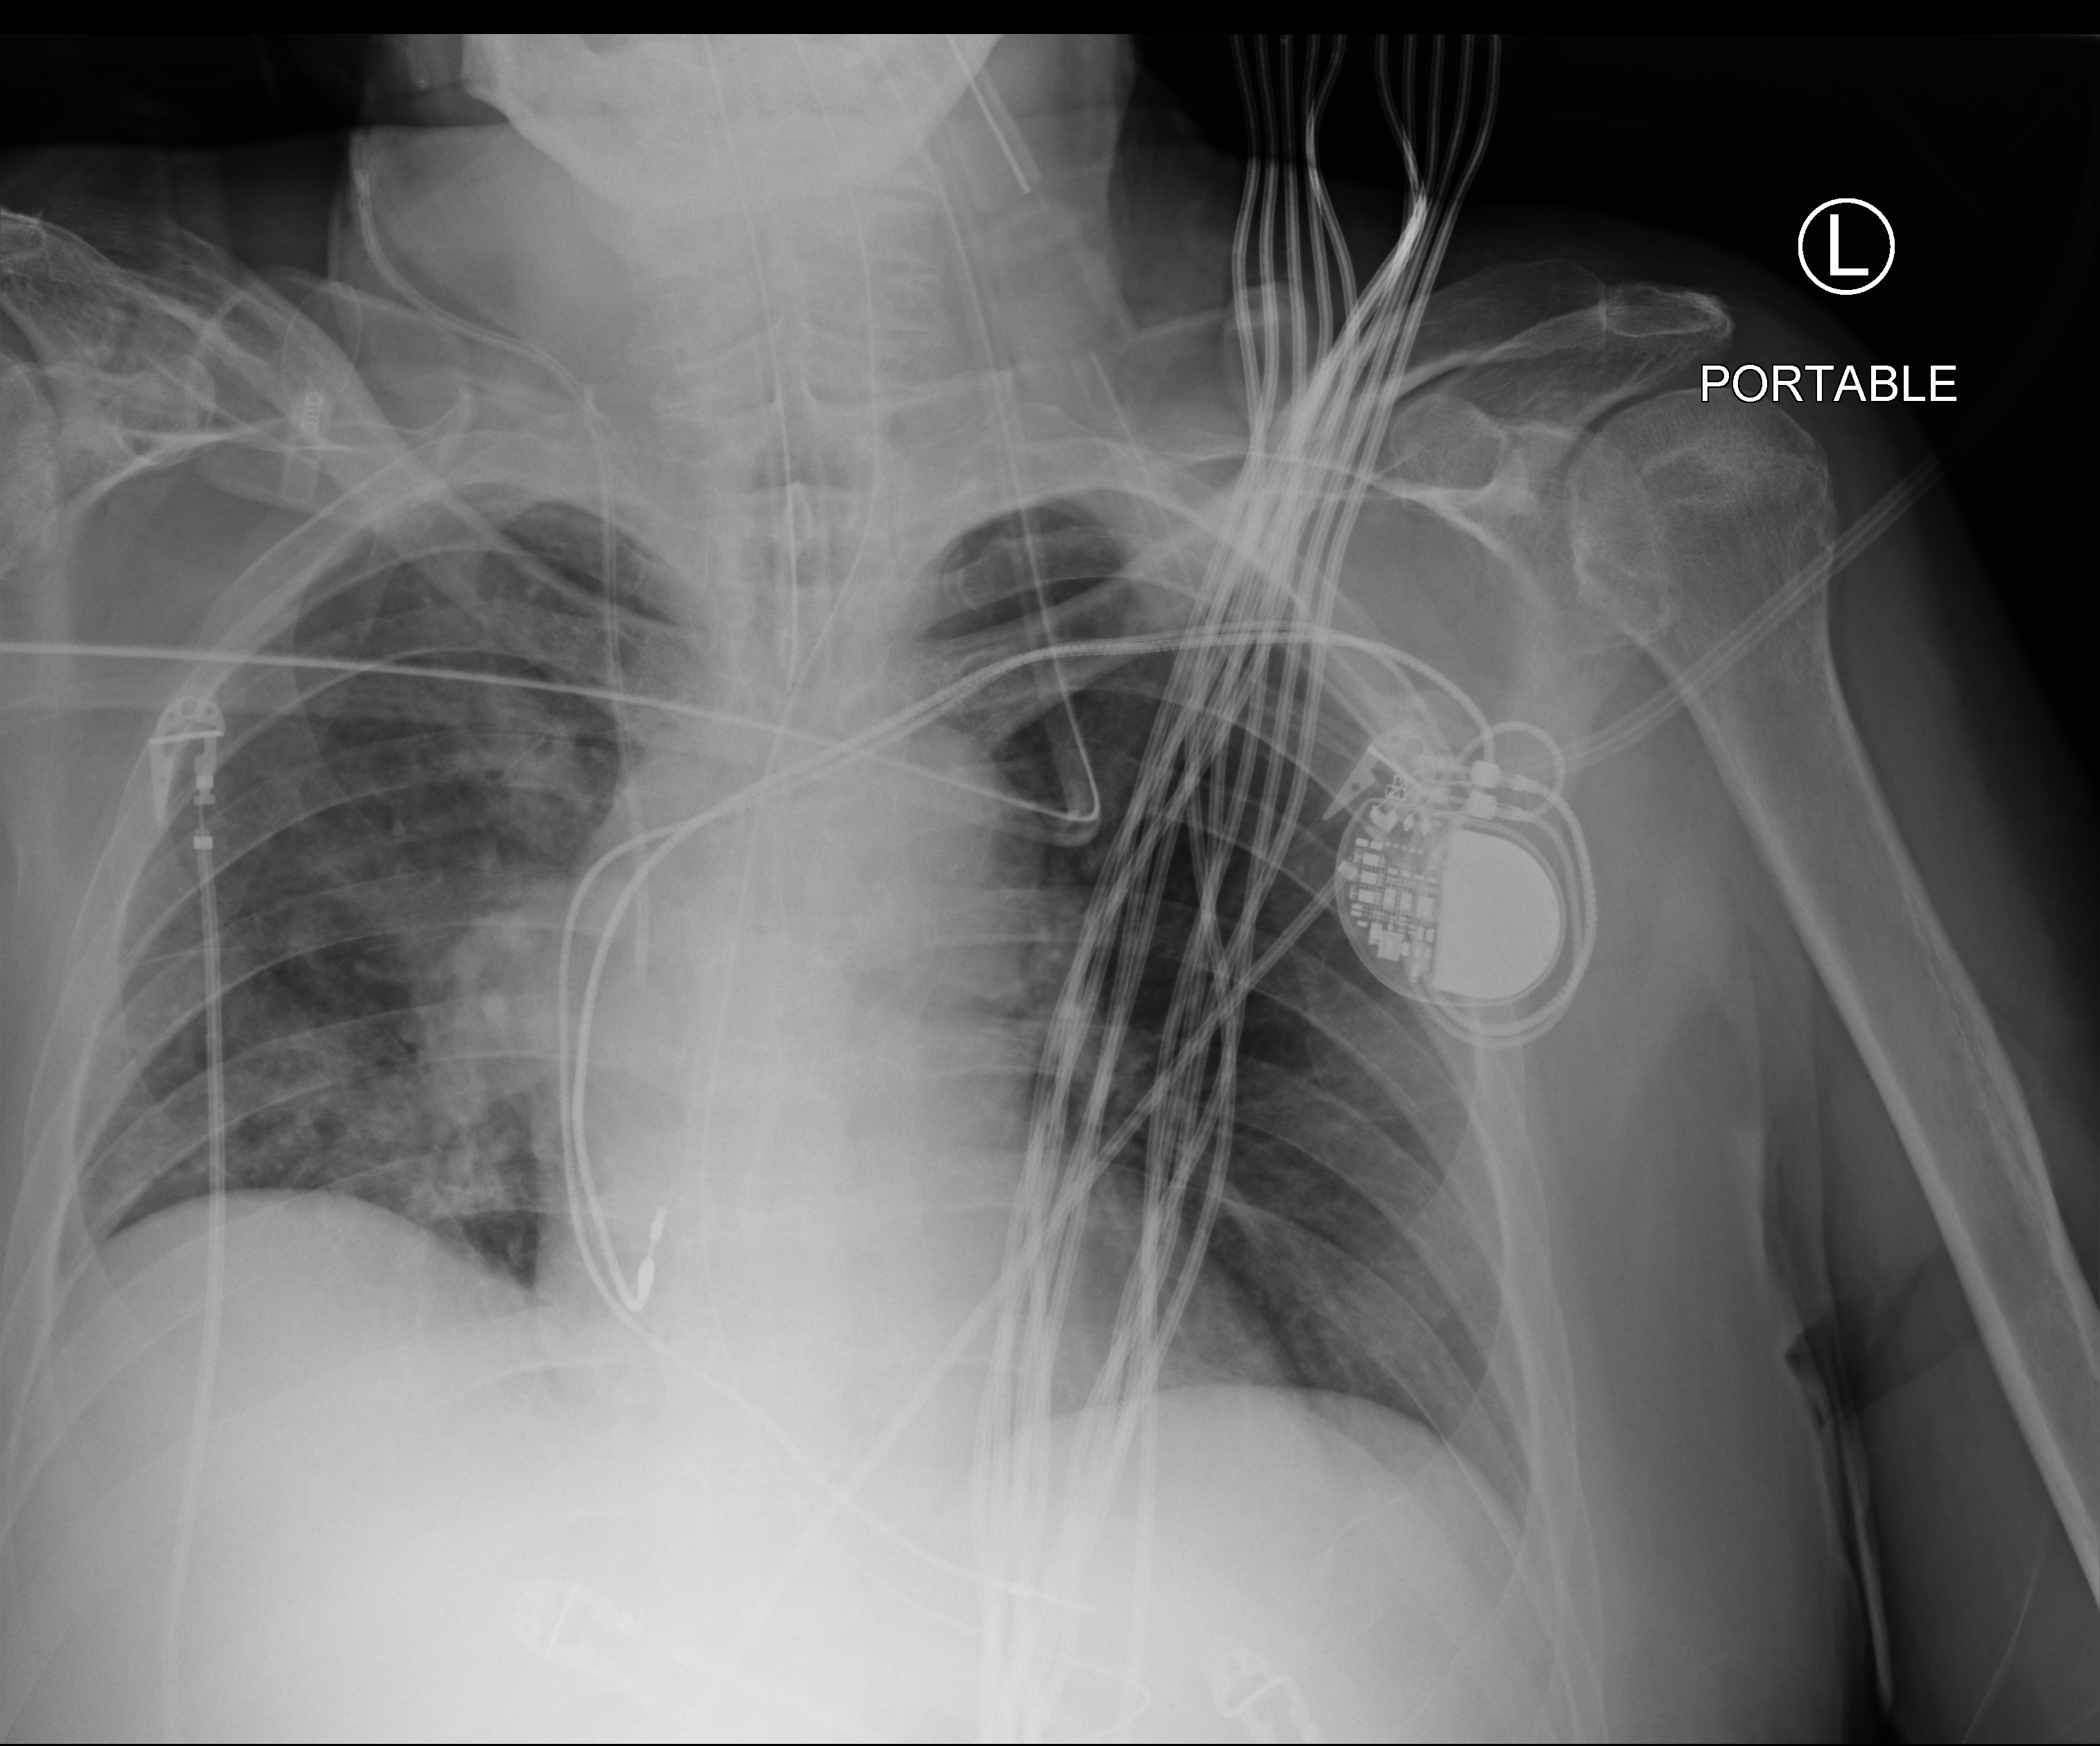
Portable chest radiograph, anteroposterior (AP) projection. Male patient hospitalised with COVID-19, age 60–74 years.
Hospital-stay facts (about this admission, not read from this image; timing relative to this image not recorded): diabetes (admission record): no.